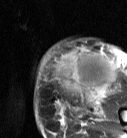
MRI of an extremity soft-tissue mass, one axial slice. Position 19 of 87 along the scan axis. T2-weighted fat-saturated. MR volume resampled by the dataset authors to the PET/CT grid (not the native acquisition matrix). 3.27 mm slice thickness. 127 × 138 image matrix, field of view 124 × 135 mm. Female patient. From the clinical record (not read from this slice): histological type: pleiomorphic leiomyosarcoma; grade: high; site of the primary tumour: left biceps.
Outlined on this slice (expert contour drawn on MRI and transferred to this co-registered scan by the dataset authors):
- gross tumour volume including surrounding oedema: bounding box <54,50,119,104> (left, top, right, bottom; pixels)
- gross tumour volume (mass): <54,50,117,95>